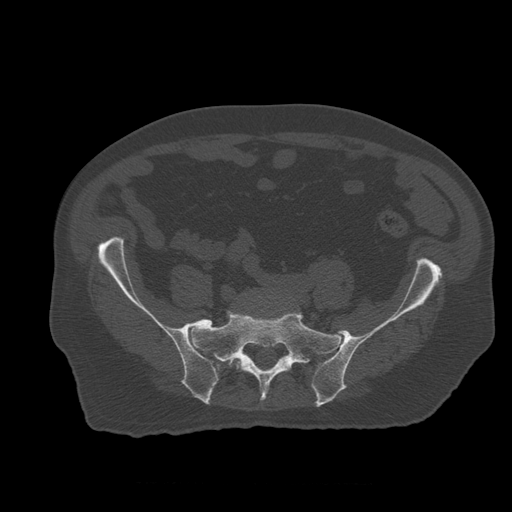
CT including the spine, one axial slice; position 123 of 399 along the scan axis; reconstruction kernel STANDARD; 120 kVp; bone window (W 1800 / L 400 HU); 1.25 mm slice thickness; 512 × 512 image matrix, field of view 407 × 407 mm. Patient age 73 years. From the clinical record (not read from this slice): primary cancer: prostate.
Structures marked on this image (semi-automatically segmented with operator editing):
- L5 vertebra: box from (x=216, y=359) to (x=233, y=382) px